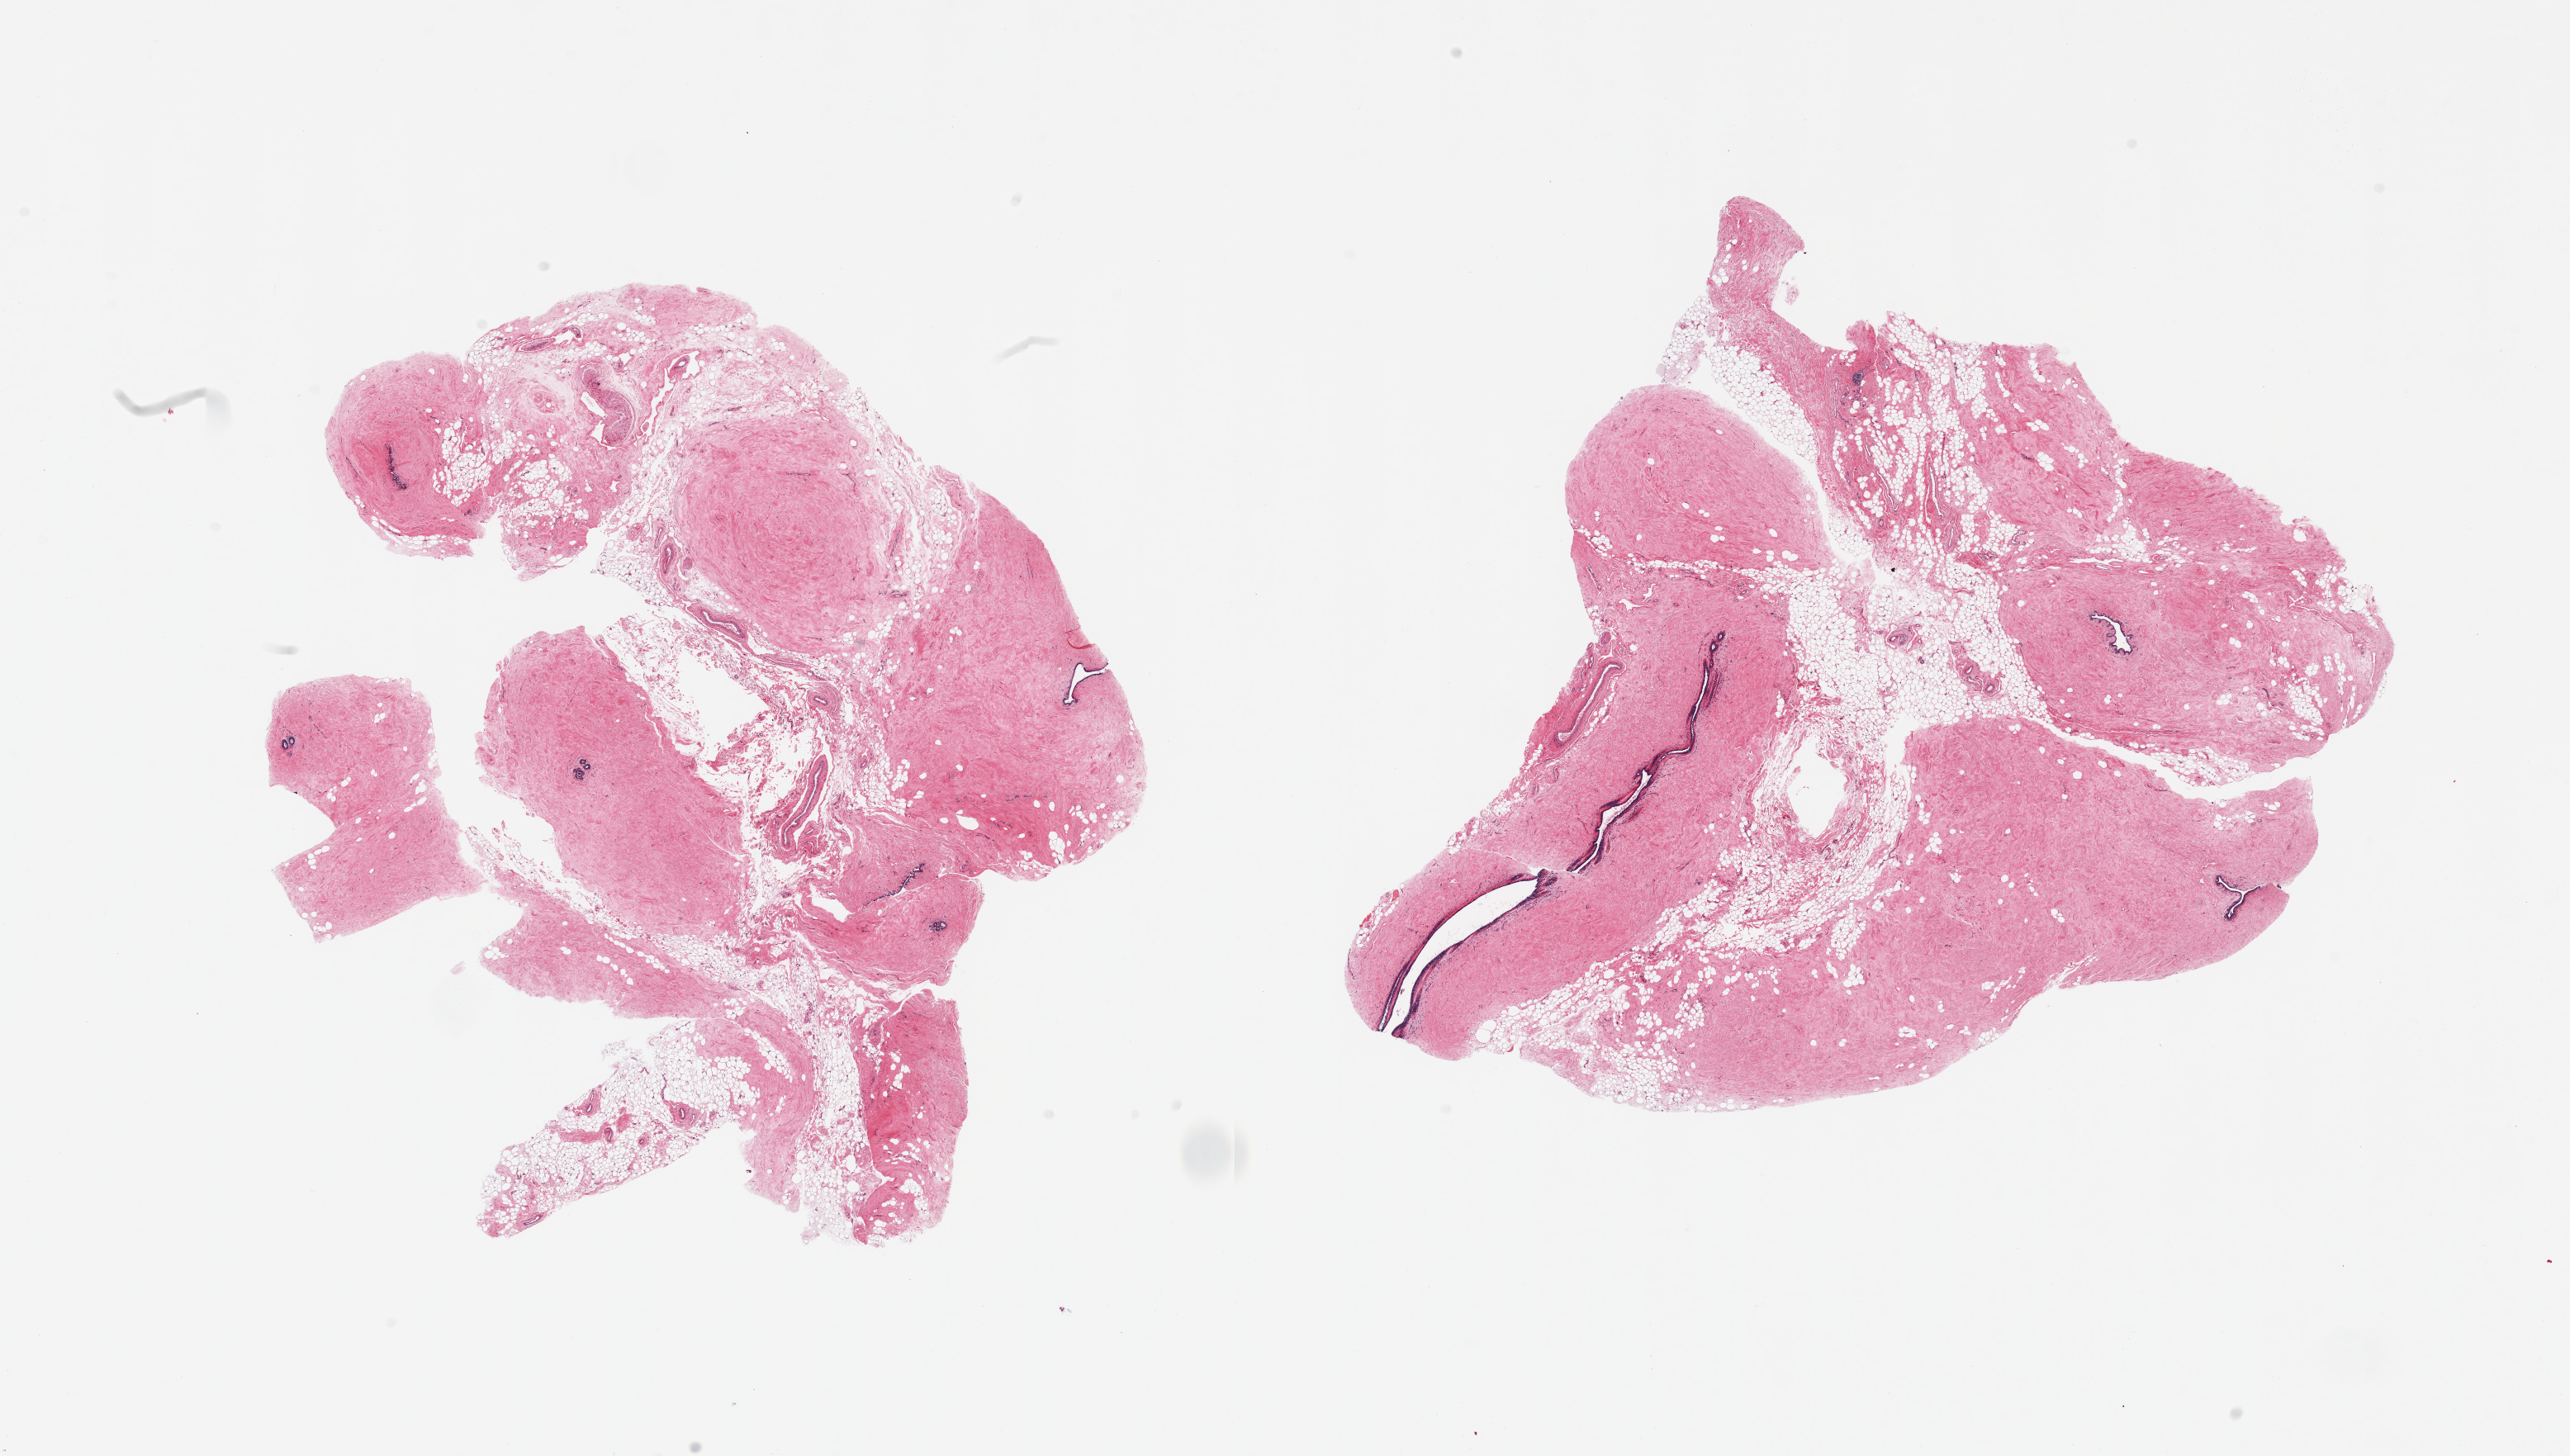
Whole-slide image, haematoxylin and eosin stain — a low-resolution overview of the entire scanned area, about 24.6 x 13.9 mm. PAXgene-fixed paraffin-embedded (PFPE) section. Sampled site (target tissue): breast. Tissue donor sample. Donor: female.
- reviewer comment on this tissue sample: 2 pieces, atrophic ductal/lobular elements